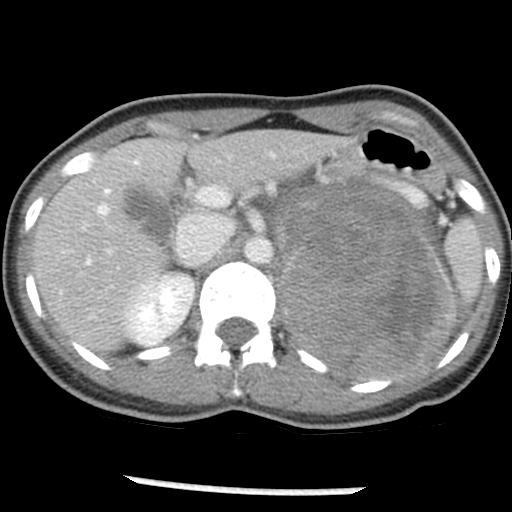
Contrast-enhanced abdominal CT, one axial slice; position 30 of 54 along the scan axis; reconstruction kernel STANDARD; 120 kVp; soft-tissue window (W 400 / L 40 HU); 512 × 512 image matrix, field of view 240 × 240 mm. Female patient, age 33 years. From the clinical record (not read from this slice): diagnosis: adrenocortical carcinoma; tumour side: left adrenal.
Structures marked on this image (semi-automatically segmented with operator editing):
- mass: box from (x=275, y=184) to (x=456, y=377) px